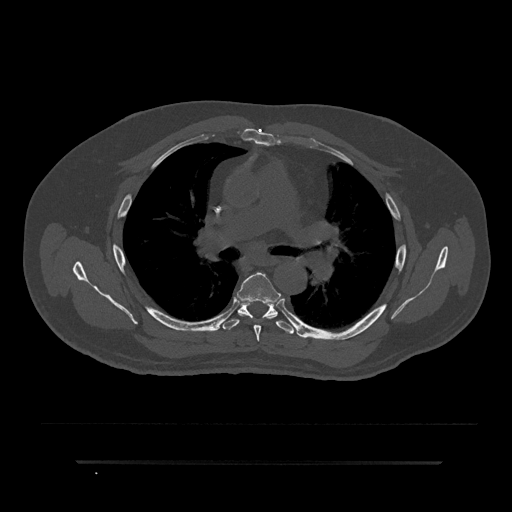
CT including the spine, one axial slice. Slice 554 of 797 in the series (ordered by position). 120 kVp. Bone window (W 1800 / L 400 HU). 0.5 mm slice thickness. 512 × 512 image matrix, field of view 464 × 464 mm. Male patient, age 59 years. From the clinical record (not read from this slice): primary cancer: bile ducts; vertebrae with lytic lesions (as recorded): T10.
Annotated regions visible in this slice (semi-automatic segmentation, software-assisted and operator-edited):
- T5 vertebra: bounding box (x1, y1, x2, y2) in pixels: (237, 272, 278, 342)
- T6 vertebra: (221, 300, 294, 334)